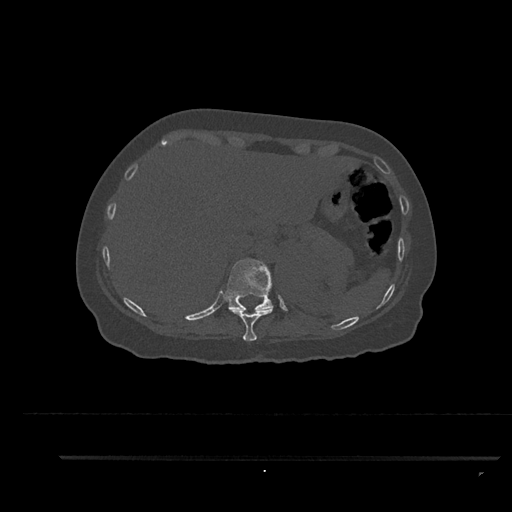
CT including the spine, one axial slice. Slice 339 of 797 in the series (ordered by position). Reconstruction kernel Br40s/3. 120 kVp. Bone window (W 1800 / L 400 HU). 512 × 512 image matrix, field of view 408 × 408 mm. Female patient, age 44 years. From the clinical record (not read from this slice): primary cancer: renal.
Annotated regions visible in this slice (semi-automatic segmentation, software-assisted and operator-edited):
- T10 vertebra: bounding box [x1, y1, x2, y2] px = [228, 307, 273, 341]
- T11 vertebra: [227, 258, 274, 311]